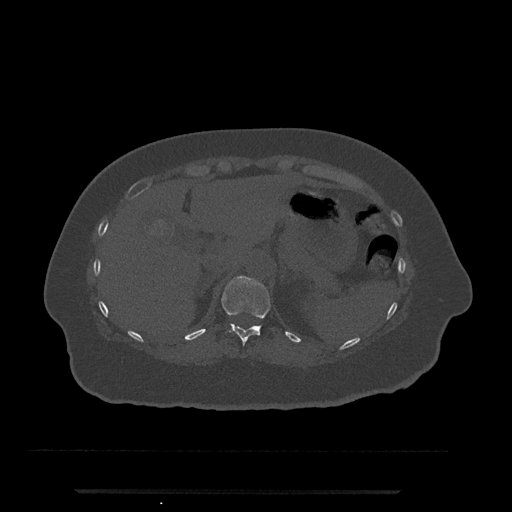
CT including the spine, one axial slice. Position 223 of 797 along the scan axis. Reconstruction kernel Br40s/3. 120 kVp. Bone window (W 1800 / L 400 HU). 0.5 mm slice thickness. 512 × 512 image matrix, field of view 440 × 440 mm. Female patient, age 51 years. From the clinical record (not read from this slice): primary cancer: neuro.
Annotated regions visible in this slice (semi-automatically segmented with operator editing):
- T11 vertebra: bounding box (x1, y1, x2, y2) in pixels: (221, 276, 271, 346)